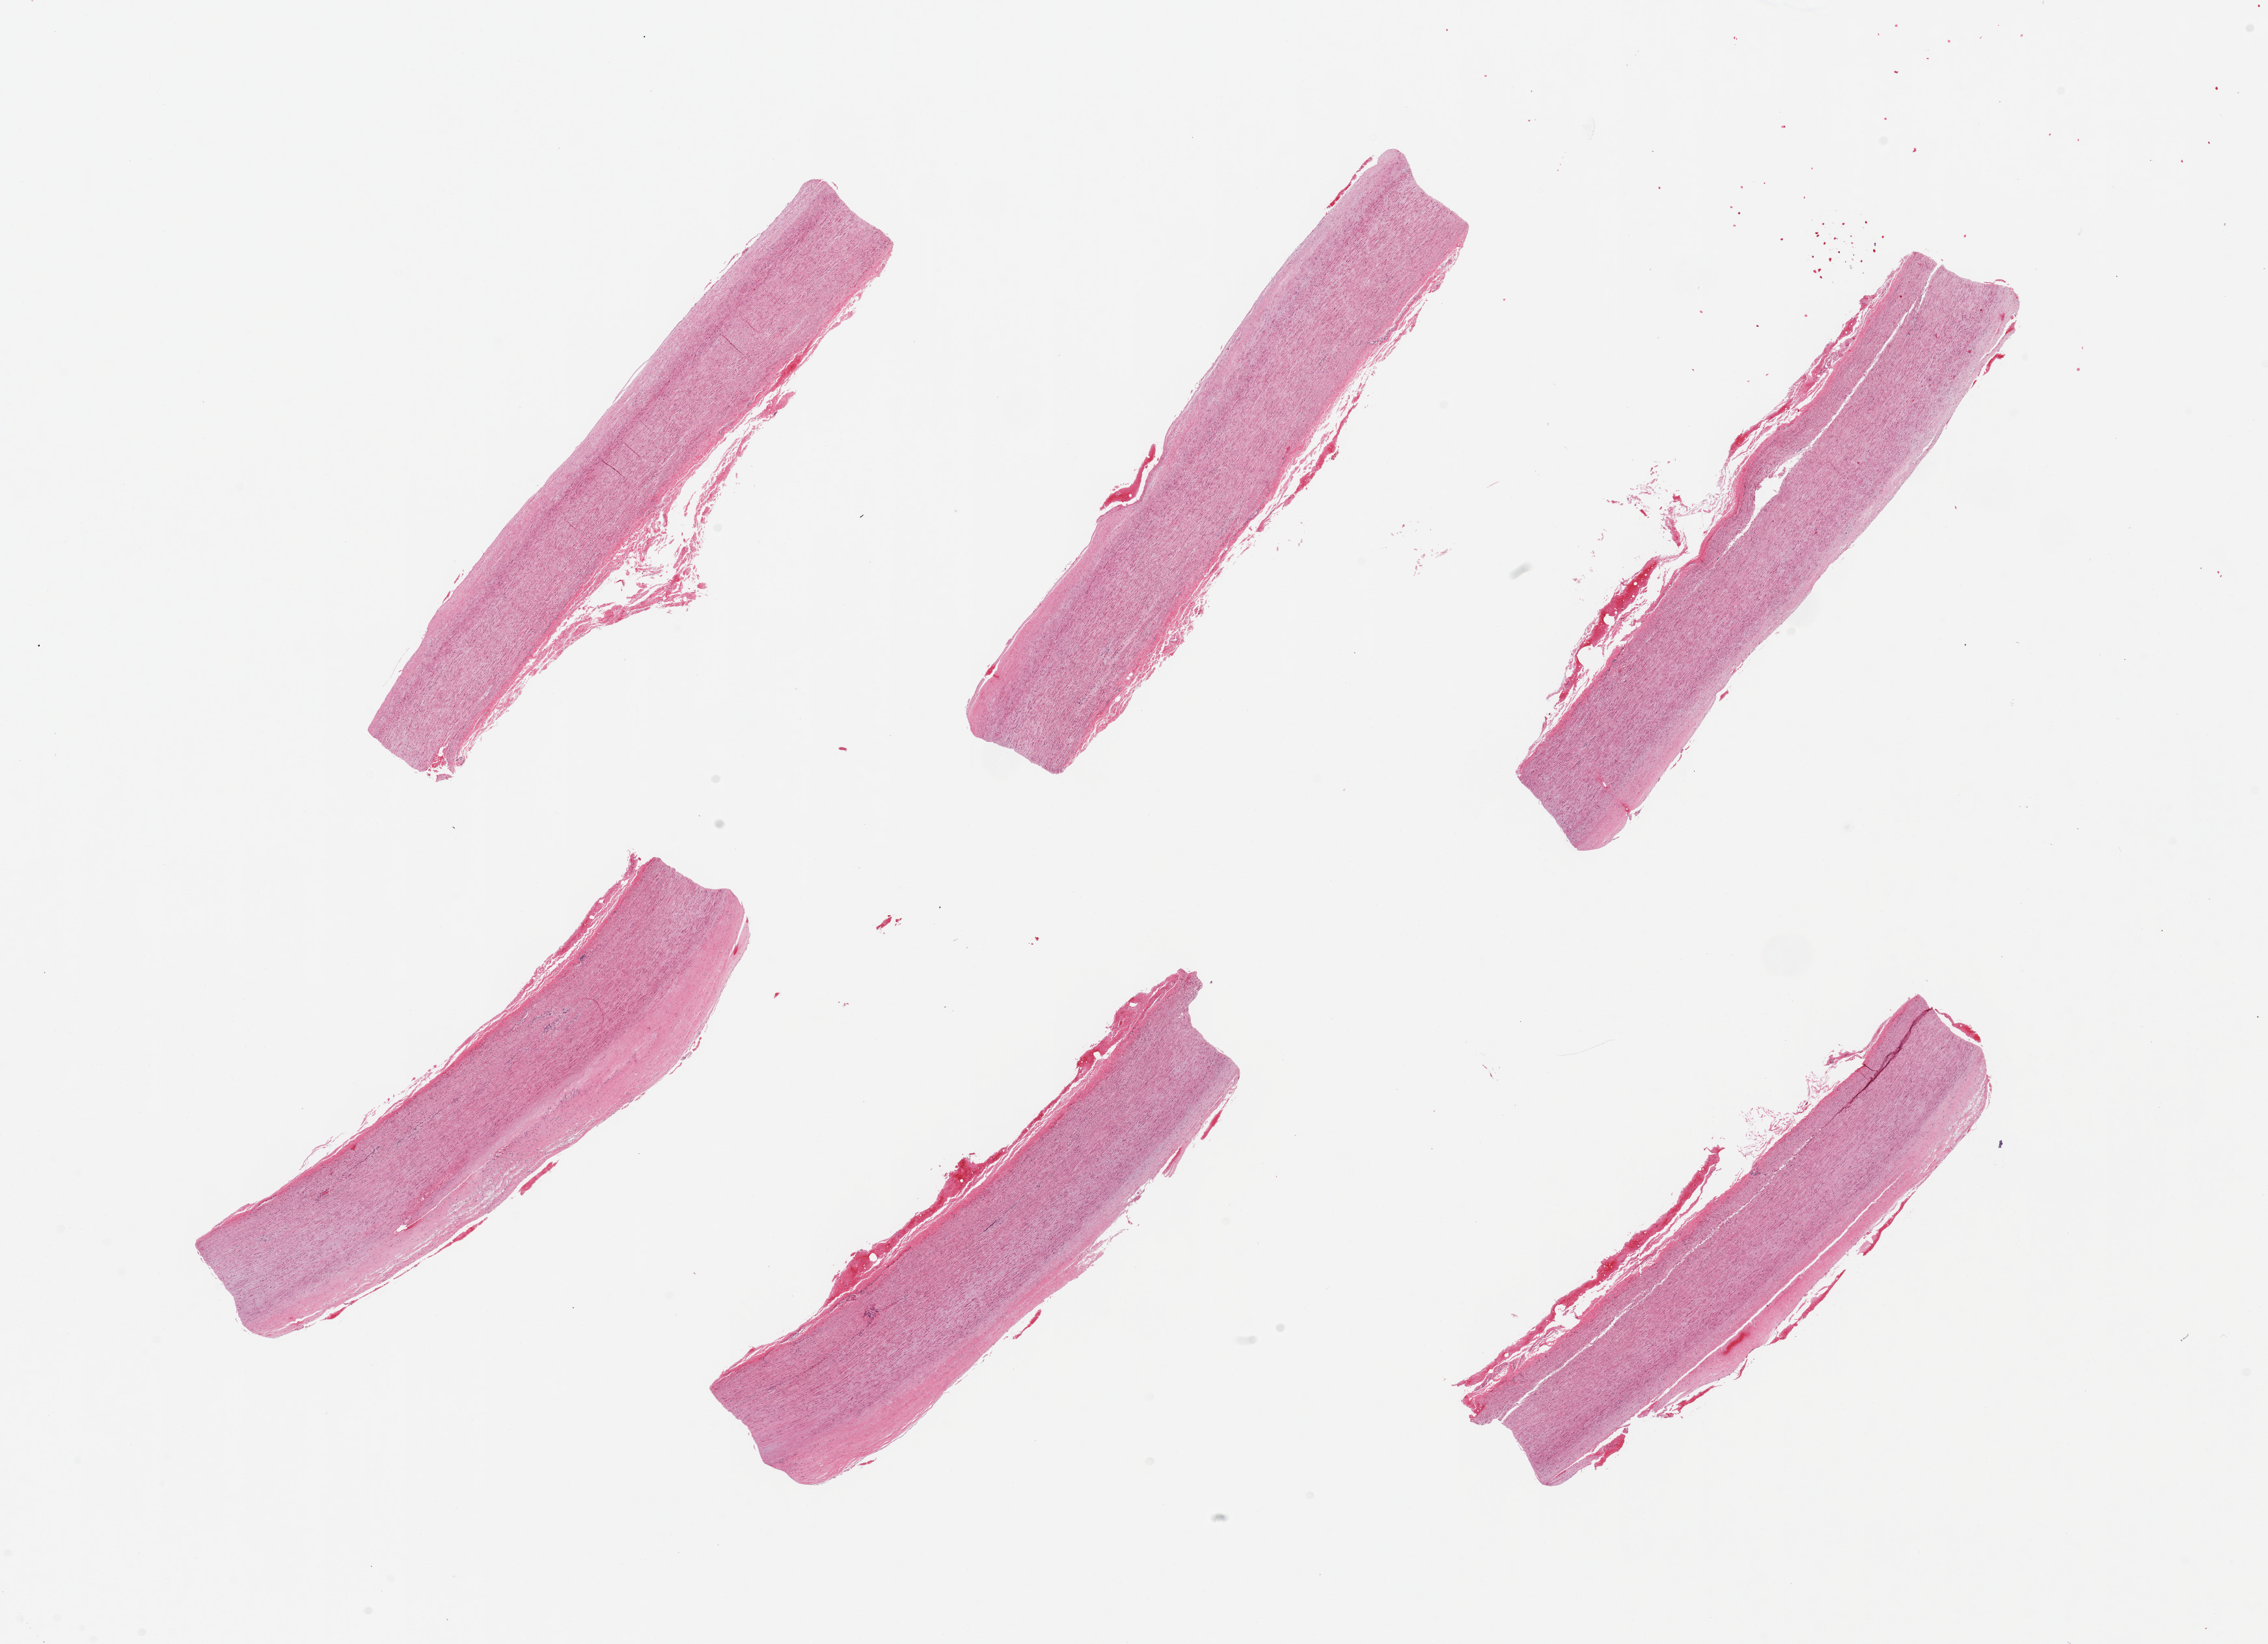
Digitized hematoxylin and eosin (H&E)-stained section — a low-resolution overview of the entire scanned area, about 27.6 x 20.0 mm (acquisition: 20x scan), PAXgene-fixed paraffin-embedded (PFPE) section, sampled site (target tissue): aorta, tissue donor sample. Female donor.
Reviewer comment on this tissue sample: 6 pieces; flat plaques up to 0.6mm thick.